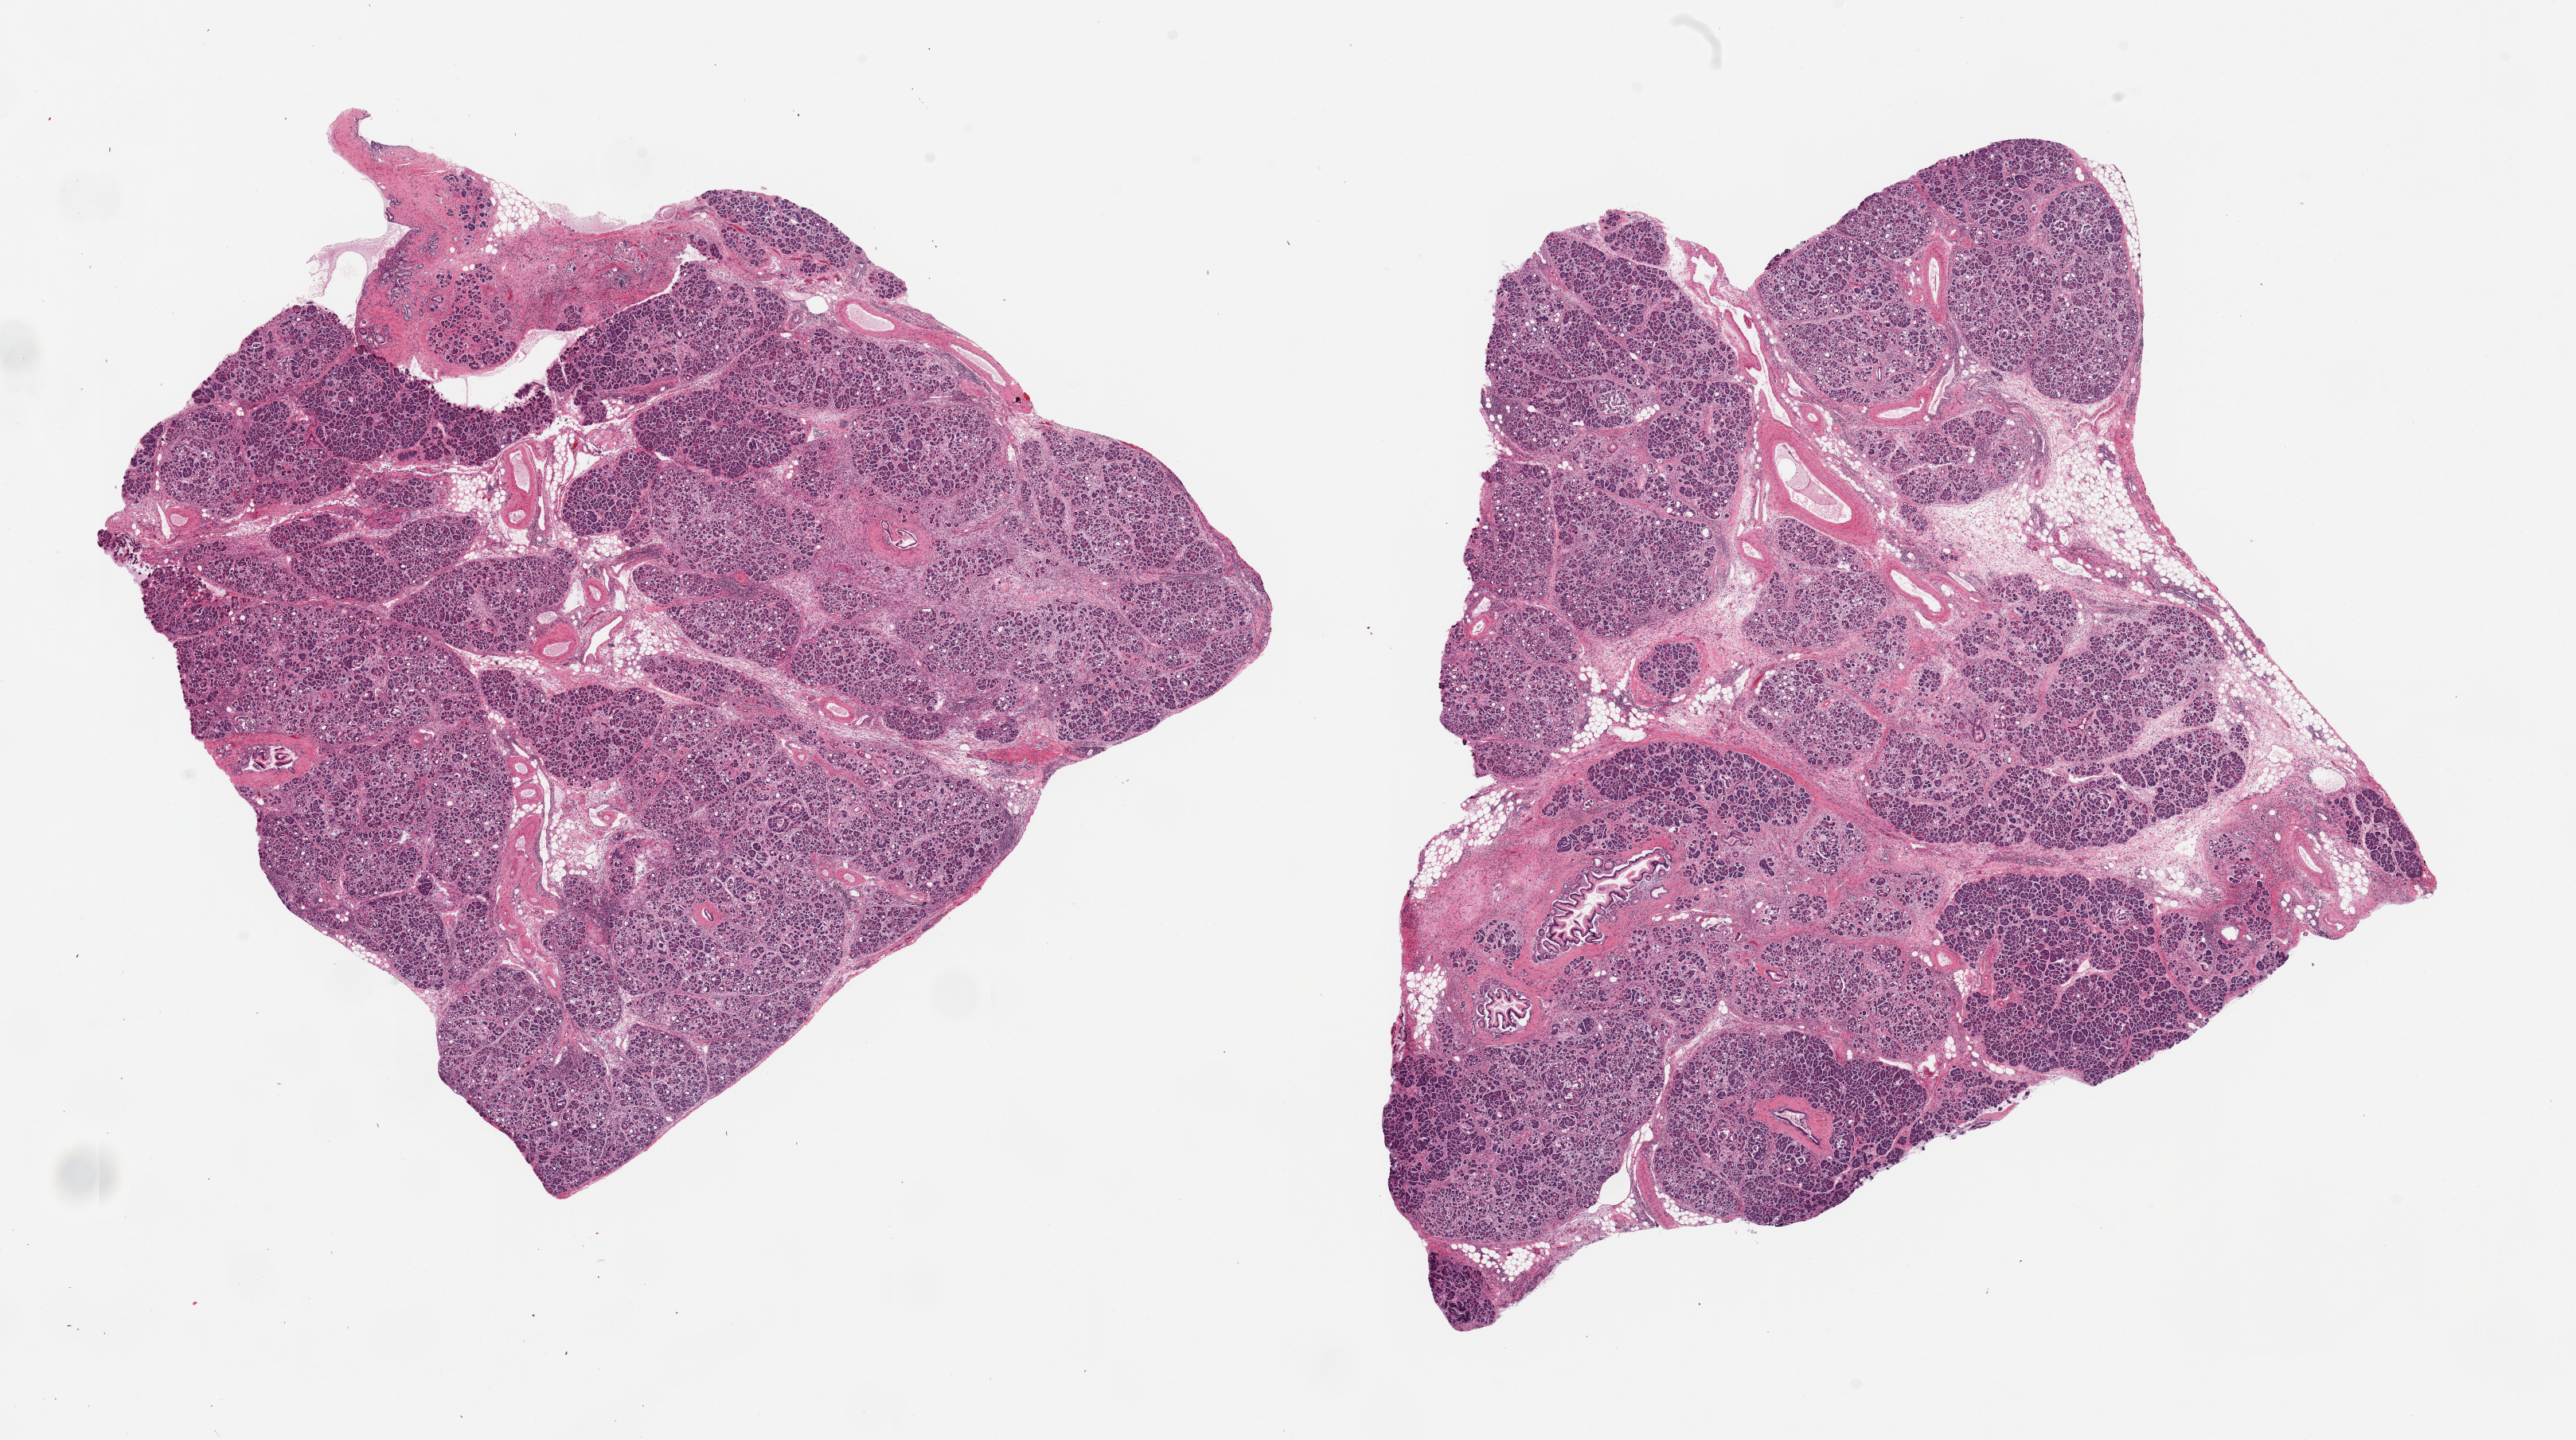
Whole-slide image, H&E stain, whole scanned area (about 25.6 x 14.3 mm, from a 20x scan) shown as a low-resolution overview; PAXgene-fixed paraffin-embedded (PFPE) section; target tissue: pancreas; donor tissue sample. Donor sex: female.
Review note (as recorded): 2 pieces, 10x9 & 11x11mm. Moderate fibrosis of endocrine and exocrine tissue. (Diabetic history.).